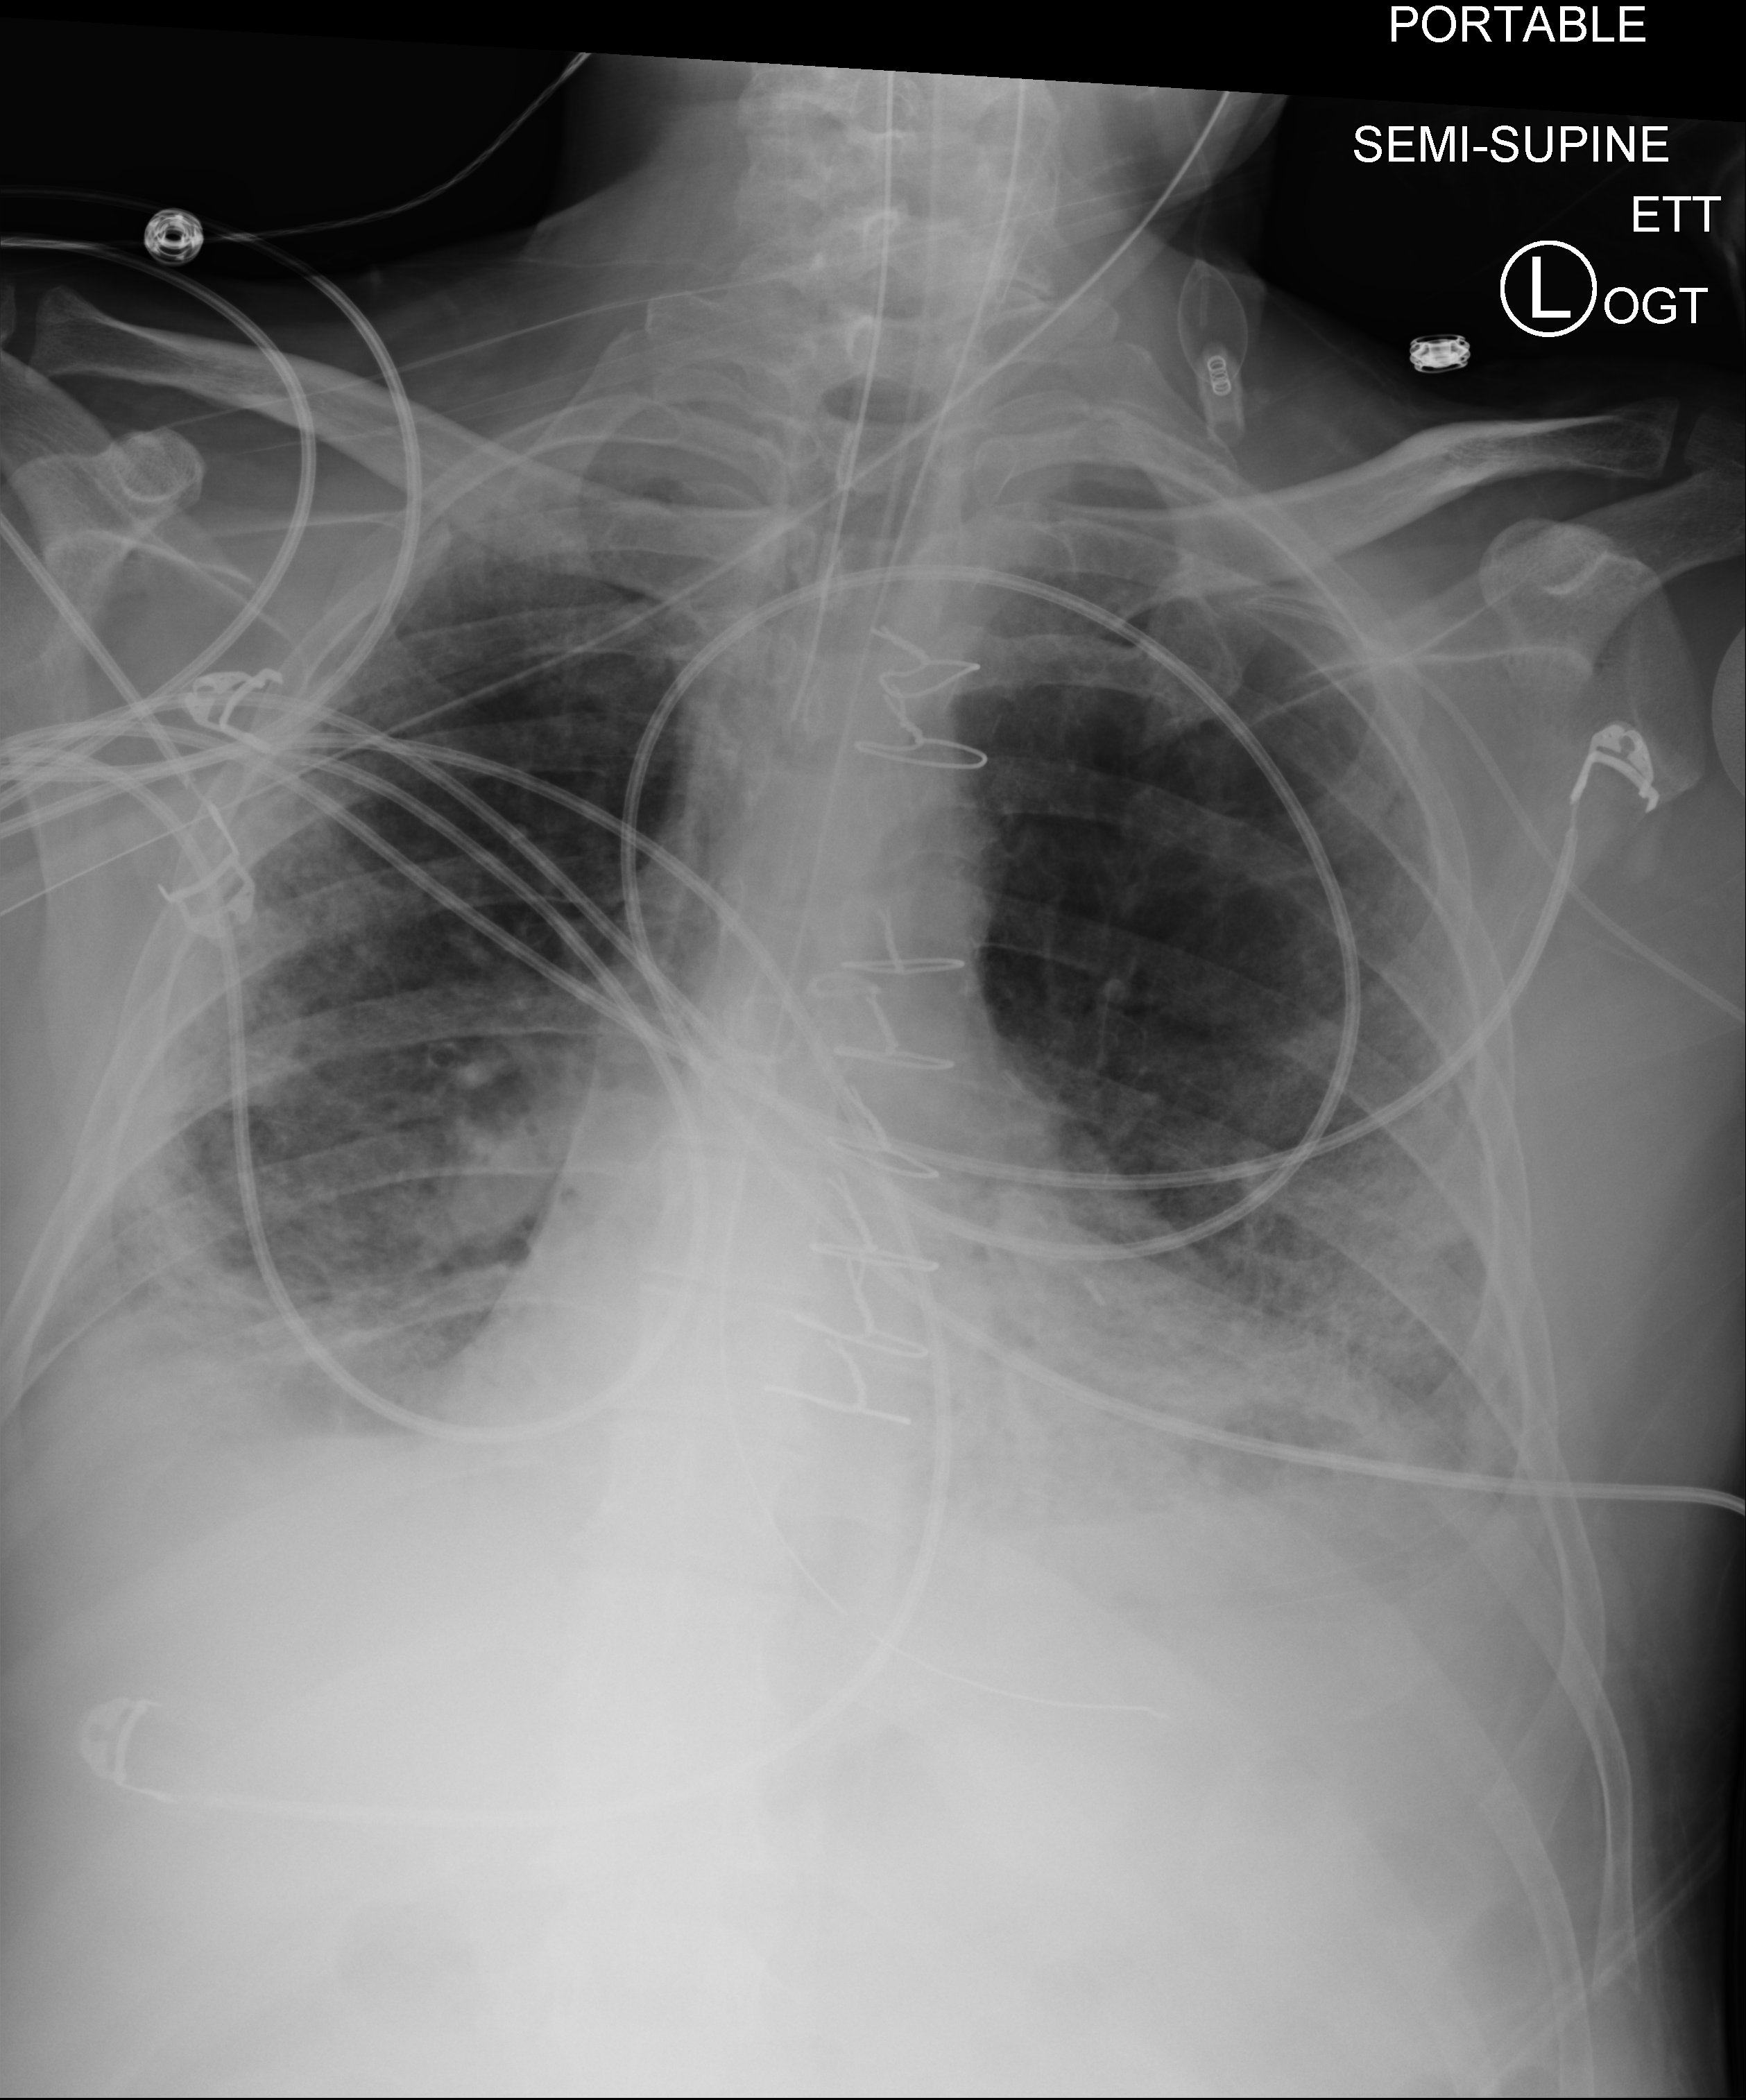
Chest X-ray (portable), anteroposterior (AP) projection. Male patient hospitalised with COVID-19, age 18–59 years.
Admission-level facts for this patient (not findings on this image; timing relative to this image not recorded):
- admitted to intensive care during this hospital stay: yes
- mechanically ventilated during this hospital stay: yes